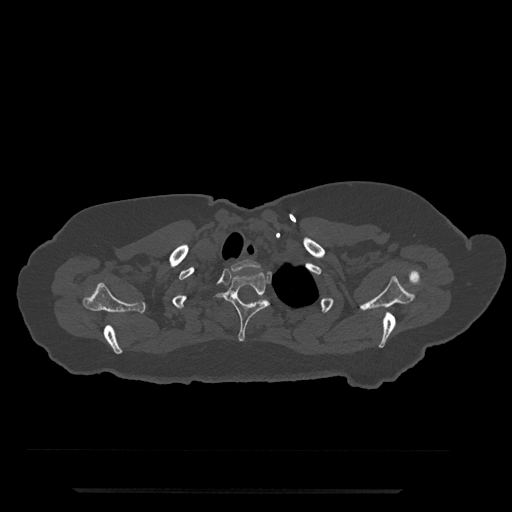
CT including the spine, one axial slice; slice 673 of 797 in the series (ordered by position); reconstruction kernel Br40s/3; 120 kVp; bone window (W 1800 / L 400 HU); 0.5 mm slice thickness; 512 × 512 image matrix, field of view 440 × 440 mm. Patient: female, 51 years. Case-level facts recorded for this patient, not image findings: primary cancer: neuro; vertebrae with lytic lesions (as recorded): T8.
Annotated regions visible in this slice (semi-automatically segmented with operator editing):
- T1 vertebra: bounding box [x1, y1, x2, y2] px = [231, 259, 260, 271]
- T2 vertebra: [216, 272, 270, 342]
- T3 vertebra: [258, 299, 266, 302]